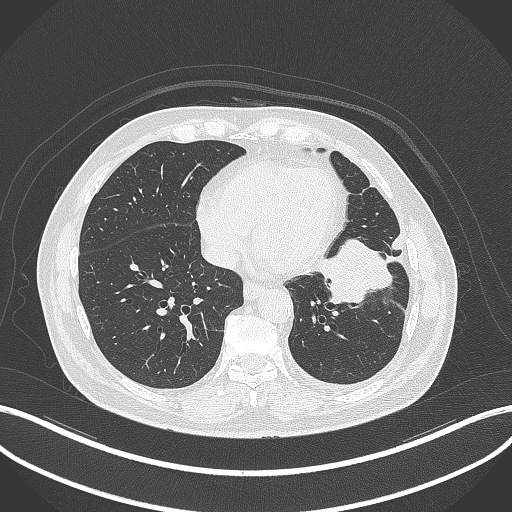
Chest CT, one axial slice. Slice 121 of 230 in the series (ordered by position). 120 kVp. Lung window (W 1500 / L -600 HU). 1 mm slice thickness. 512 × 512 image matrix. Male patient, age 68 years. From the clinical record (not read from this slice): clinical TNM (as recorded): T2b N0 M0.
Annotated regions visible in this slice (bounding box drawn by a radiologist):
- lung tumour (recorded histology: squamous cell carcinoma): box from (x=313, y=224) to (x=397, y=308) px